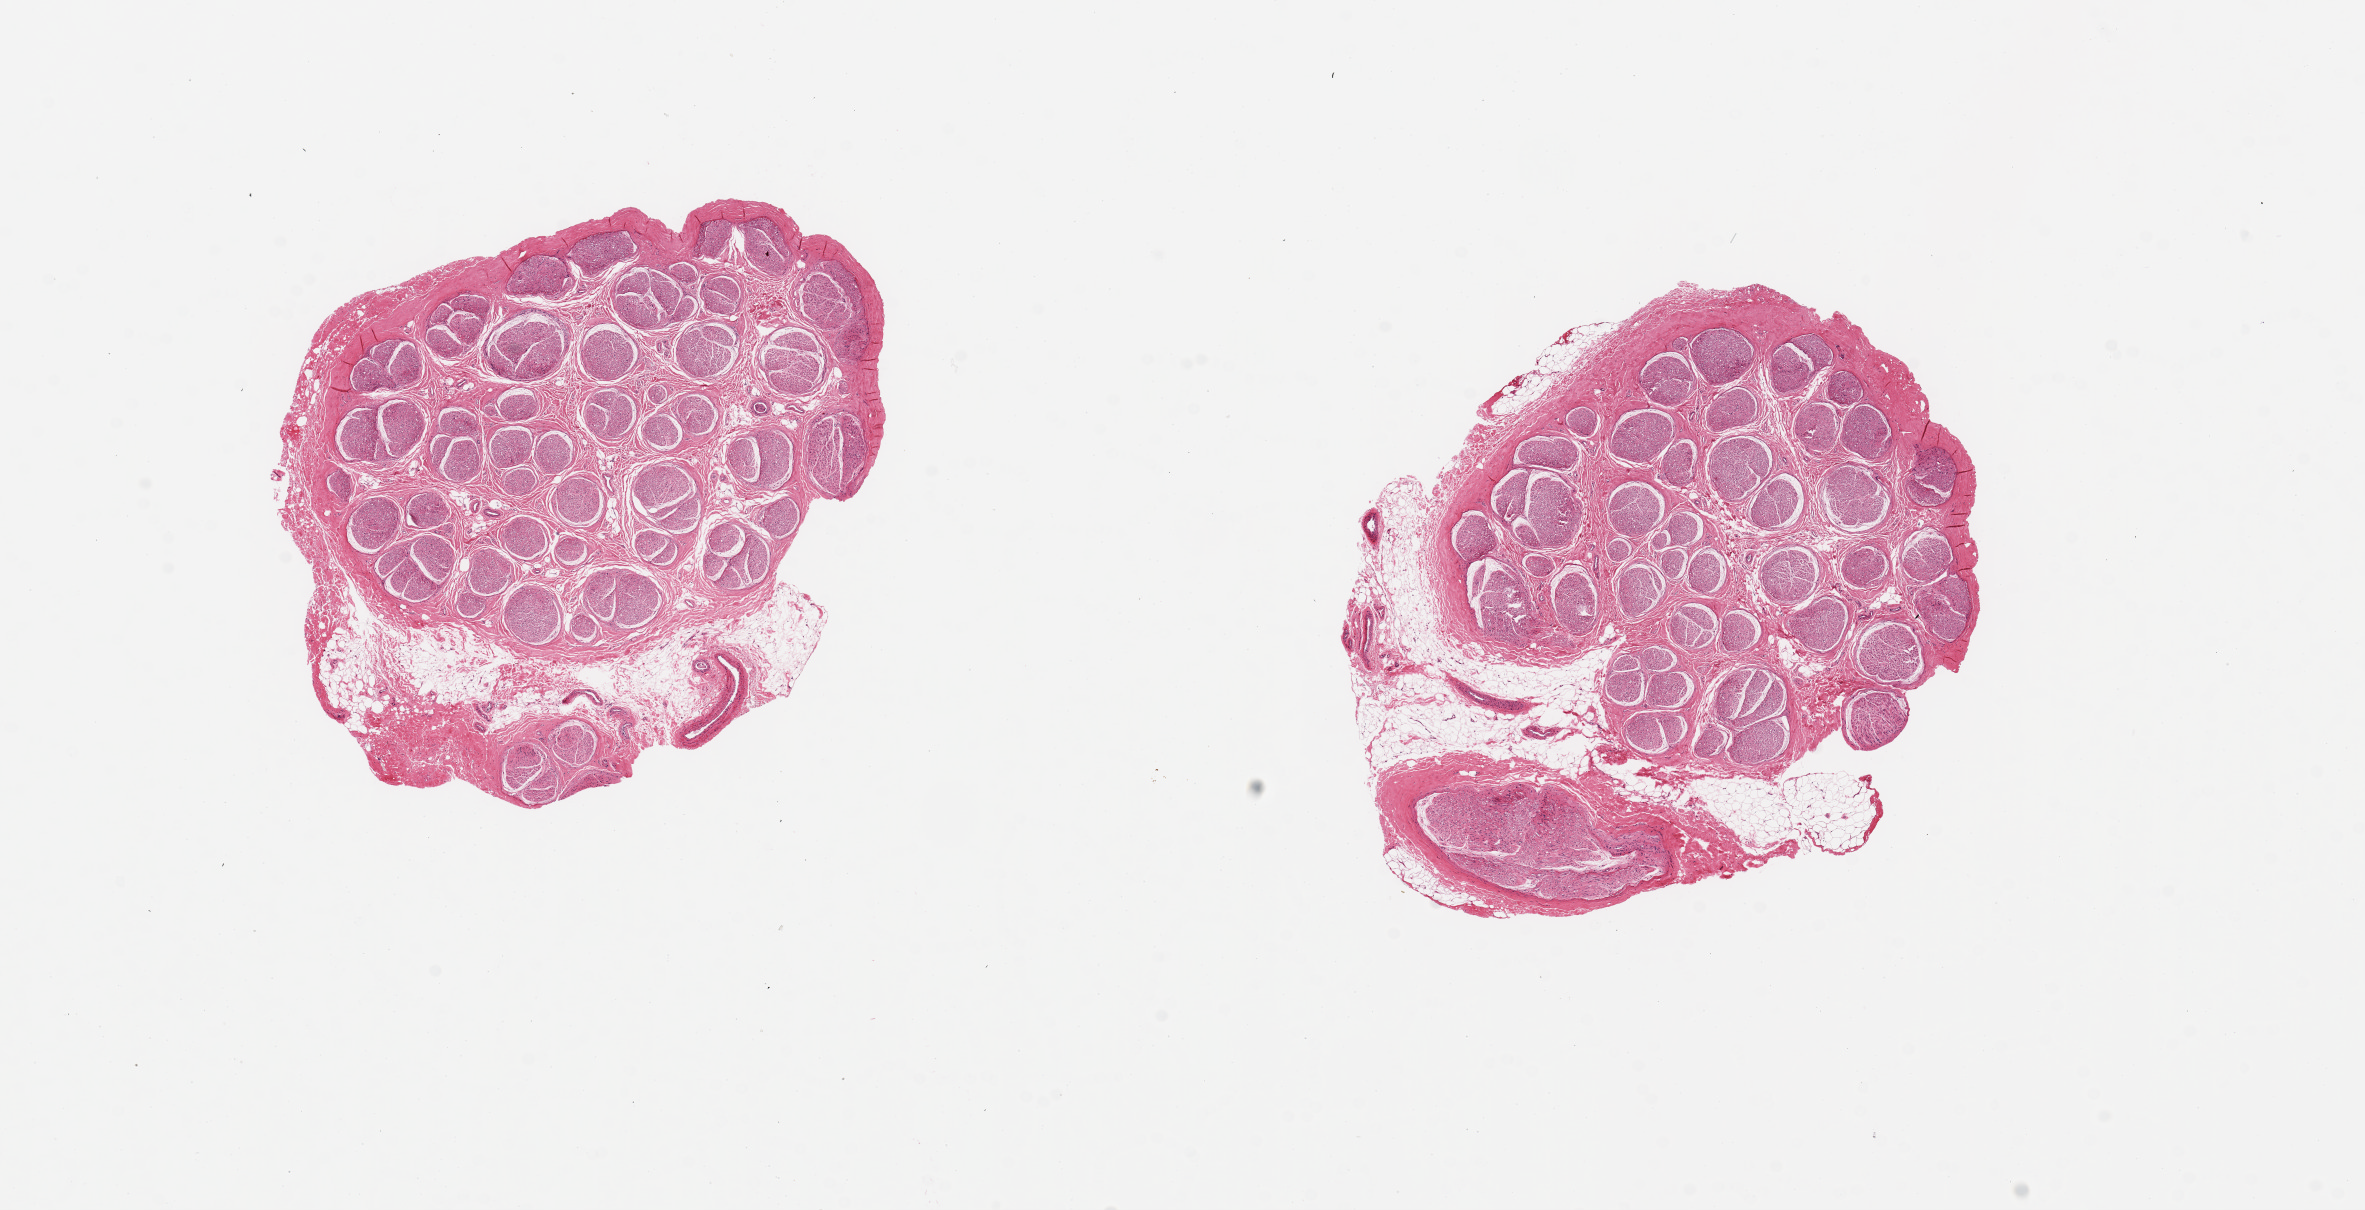
H&E whole-slide image, brightfield, whole scanned area (about 18.7 x 9.6 mm) shown as a low-resolution overview, PAXgene-fixed paraffin-embedded (PFPE) section, target tissue: tibial nerve, donor tissue sample. Donor sex: male.
Reviewer comment on this tissue sample: 2 pieces, ~5mm d. Clean specimens, focal interstitial fat.